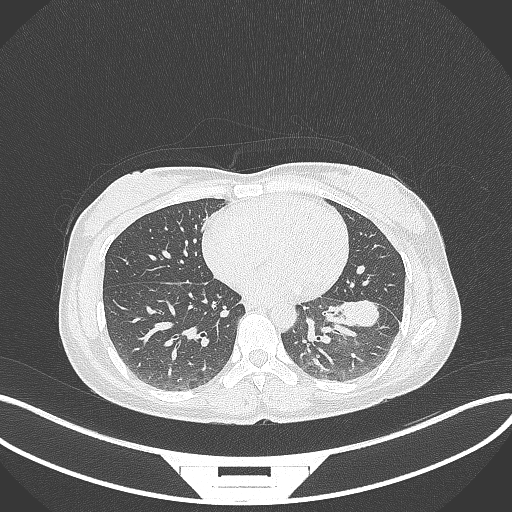
Chest CT, one axial slice. Position 28 of 244 along the scan axis. Lung window (W 1500 / L -600 HU). 1 mm slice thickness. 512 × 512 image matrix, field of view 400 × 400 mm. Patient: female, 41 years. Case-level facts recorded for this patient, not image findings: clinical TNM (as recorded): T2a N3 M1b.
Outlined on this slice (rectangle marked by the reading radiologist):
- lung tumour (recorded histology: adenocarcinoma): box from (x=324, y=294) to (x=383, y=333) px